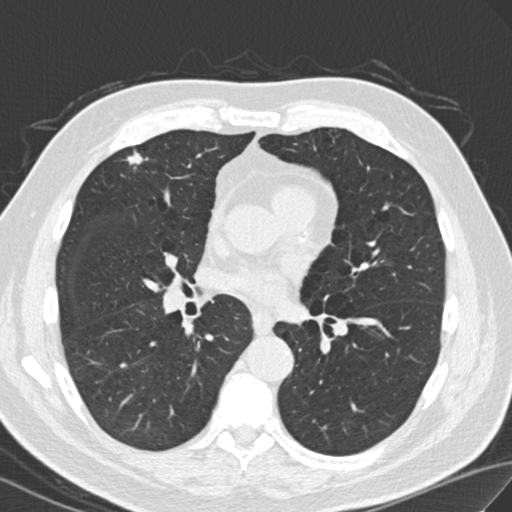
Low-dose screening chest CT, one axial slice. Position 83 of 171 along the scan axis. Reconstruction kernel B30f. 120 kVp. Lung window (W 1500 / L -600 HU). 2 mm slice thickness. 512 × 512 image matrix, field of view 352 × 352 mm.
Structures marked on this image (outlined manually by an expert reader):
- lesion 1 (tumor, upper lobe of right lung): bounding box [x1, y1, x2, y2] px = [126, 151, 144, 165]